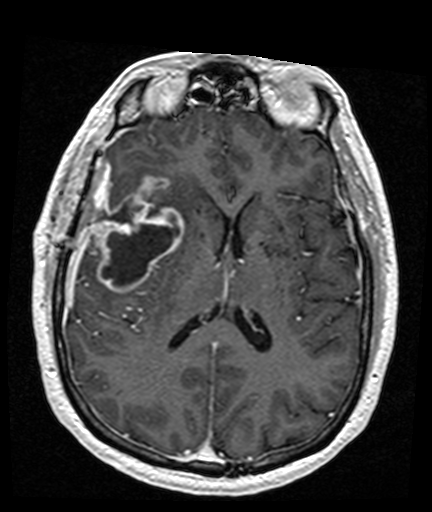
Brain MRI from a brain-tumour surgery series, one axial slice. Slice 75 of 176 in the series (ordered by position). T1-weighted post-contrast. 432 × 512 image matrix, field of view 194 × 230 mm. From the clinical record (not read from this slice): histopathology: Glioblastoma; WHO grade: 4; IDH mutation: no; tumour location: Right Frontal Temporal, Posterior Sylvian Fissure.
Structures marked on this image (outlined manually by an expert reader):
- tumour: bounding box [x1, y1, x2, y2] px = [92, 176, 184, 294]